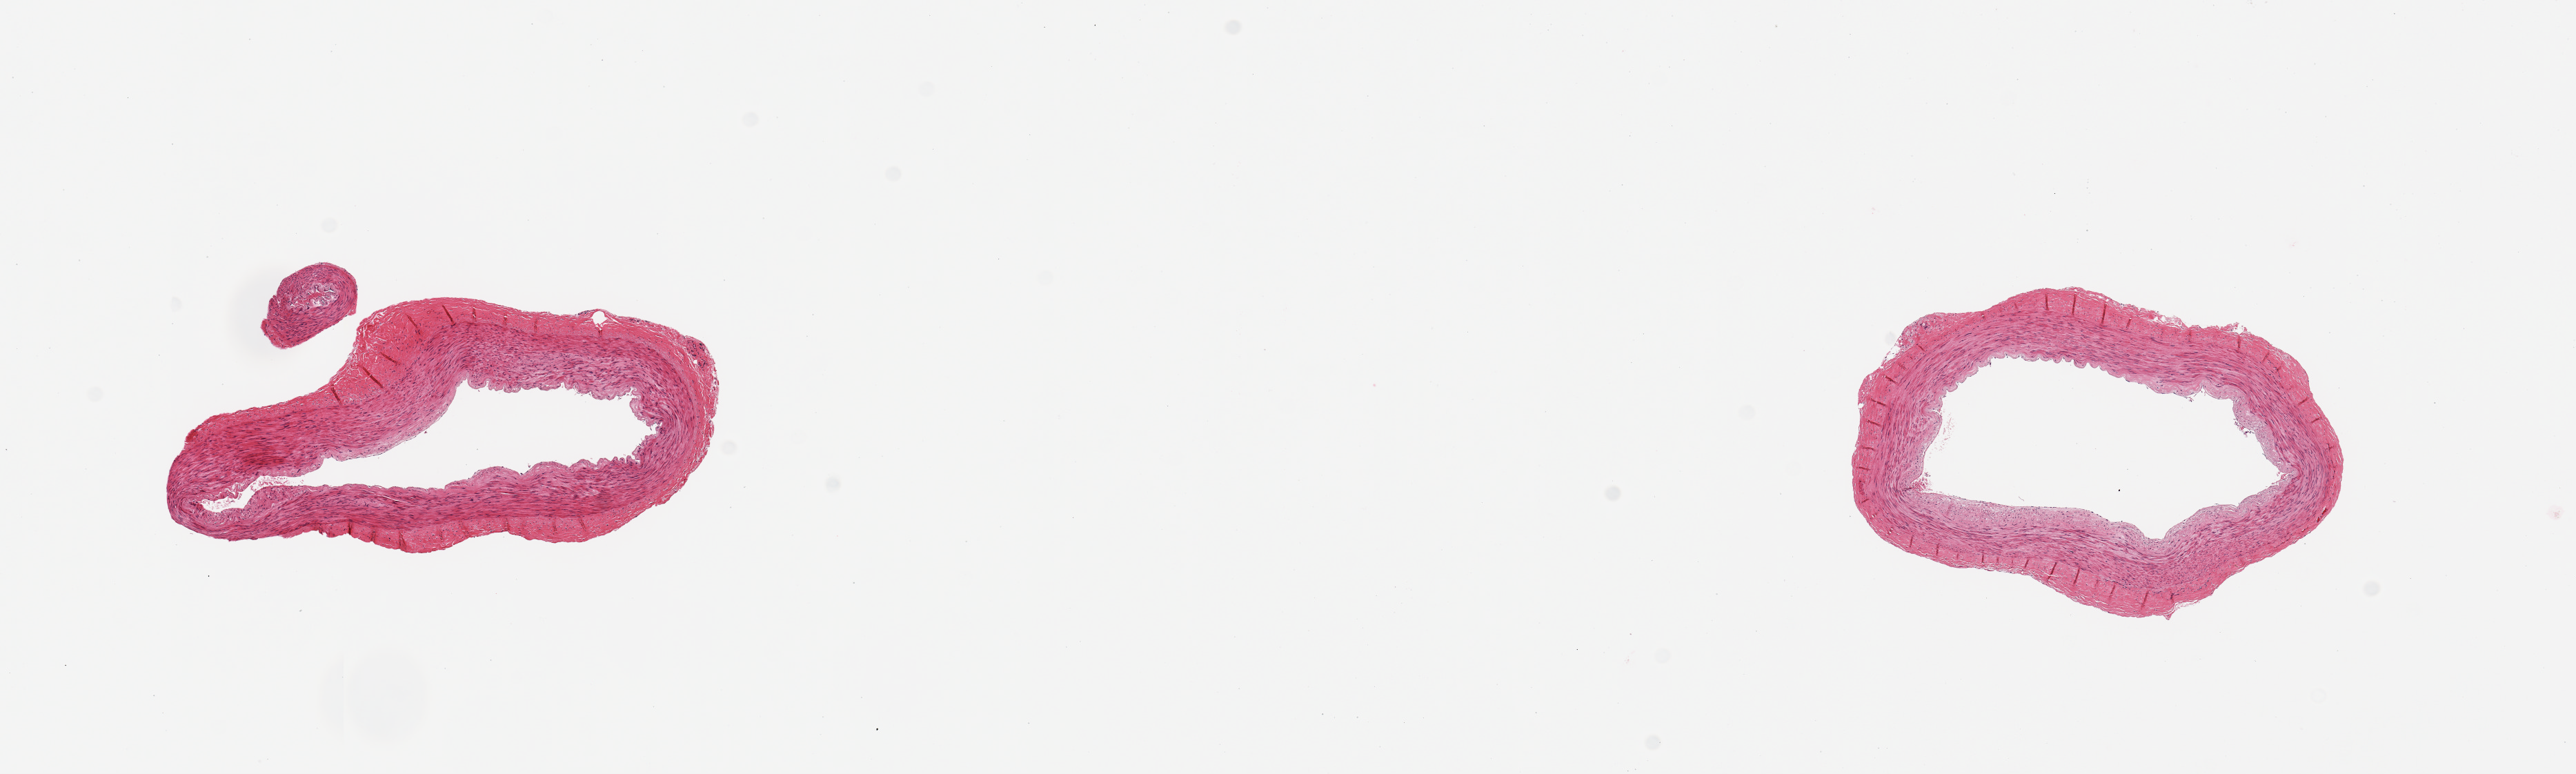
Whole-slide image, H&E stain, brightfield — shown as a low-resolution overview of the whole scanned area (about 14.8 x 4.4 mm); PAXgene-fixed, paraffin-embedded tissue; sampled site (target tissue): tibial artery; donor tissue sample. Donor sex: male.
Reviewer comment on this tissue sample: 2 pieces, no adherent fat/ atherosis.